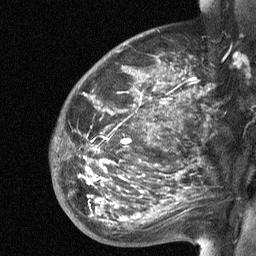
Breast MRI (dynamic contrast-enhanced), one sagittal slice. Dynamic contrast-enhanced study with each time point stored as its own series, time point 2 of 3 at this slice position (early post-contrast, ordered by acquisition time). 1.5 T. TE 4.8 ms, TR 27 ms. 2 mm slice thickness. 256 × 256 image matrix, field of view 200 × 200 mm. Patient: female, 50 years. Case-level facts recorded for this patient, not image findings: setting: breast cancer imaged before/during neoadjuvant chemotherapy; receptor status: HER2-positive.
Annotated regions visible in this slice (semi-automatic segmentation, software-assisted and operator-edited):
- analysis volume of interest (the breast-tissue region the enhancement analysis was run in; not a lesion): bounding box [x1, y1, x2, y2] px = [53, 91, 204, 227]
- tumour enhancement mask (voxels above the 90 % enhancement threshold inside the analysis volume of interest): [87, 161, 124, 200]